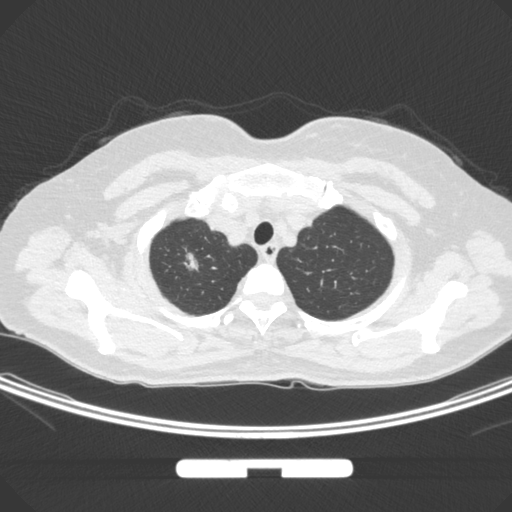
Chest CT, one axial slice. Slice 257 of 295 in the series (ordered by position). Lung window (W 1500 / L -600 HU). 1 mm slice thickness. 512 × 512 image matrix, field of view 369 × 369 mm. Female patient, age 58 years. Case-level facts recorded for this patient, not image findings: clinical TNM (as recorded): T1b N0 M0; histopathological grade: G2-3.
Structures marked on this image (rectangle marked by the reading radiologist):
- lung tumour (recorded histology: adenocarcinoma): bounding box (x1, y1, x2, y2) in pixels: (178, 245, 200, 279)